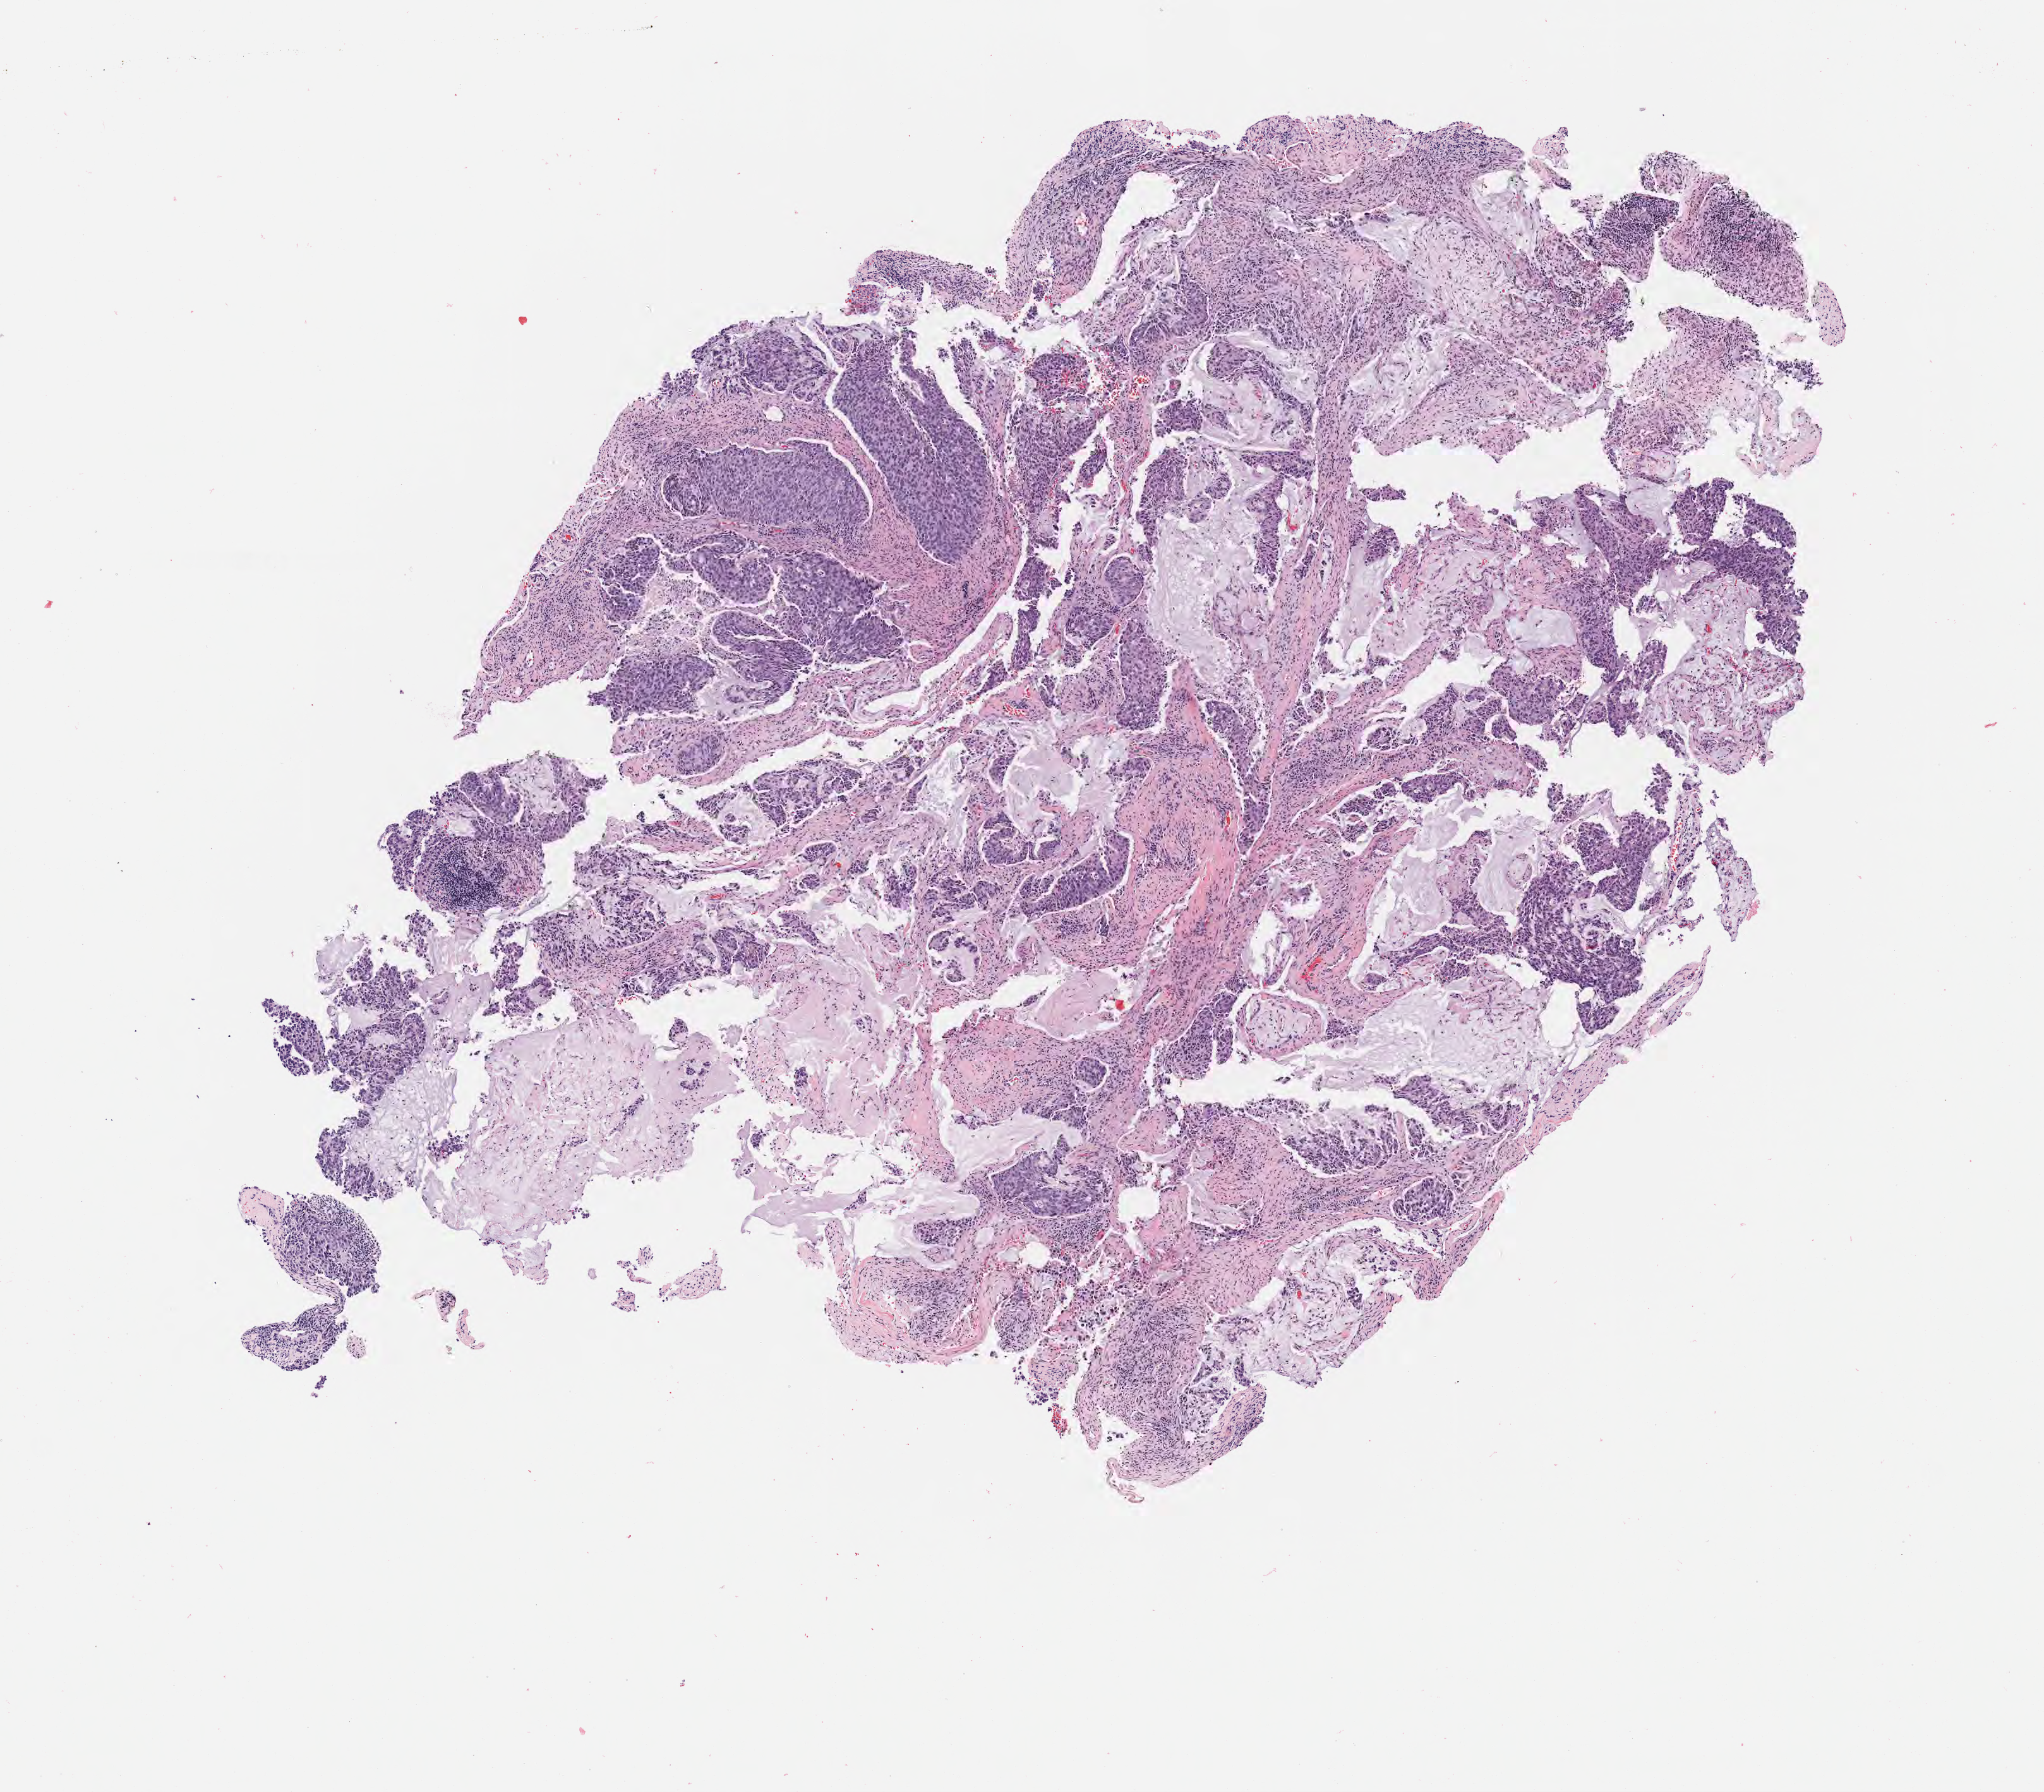
Haematoxylin and eosin whole-slide image, a low-resolution overview of the entire scanned area, about 6.5 x 5.7 mm. Tumor tissue. Site: cervix. Patient female; 43 years old.
Diagnosis: Adenocarcinoma, NOS.